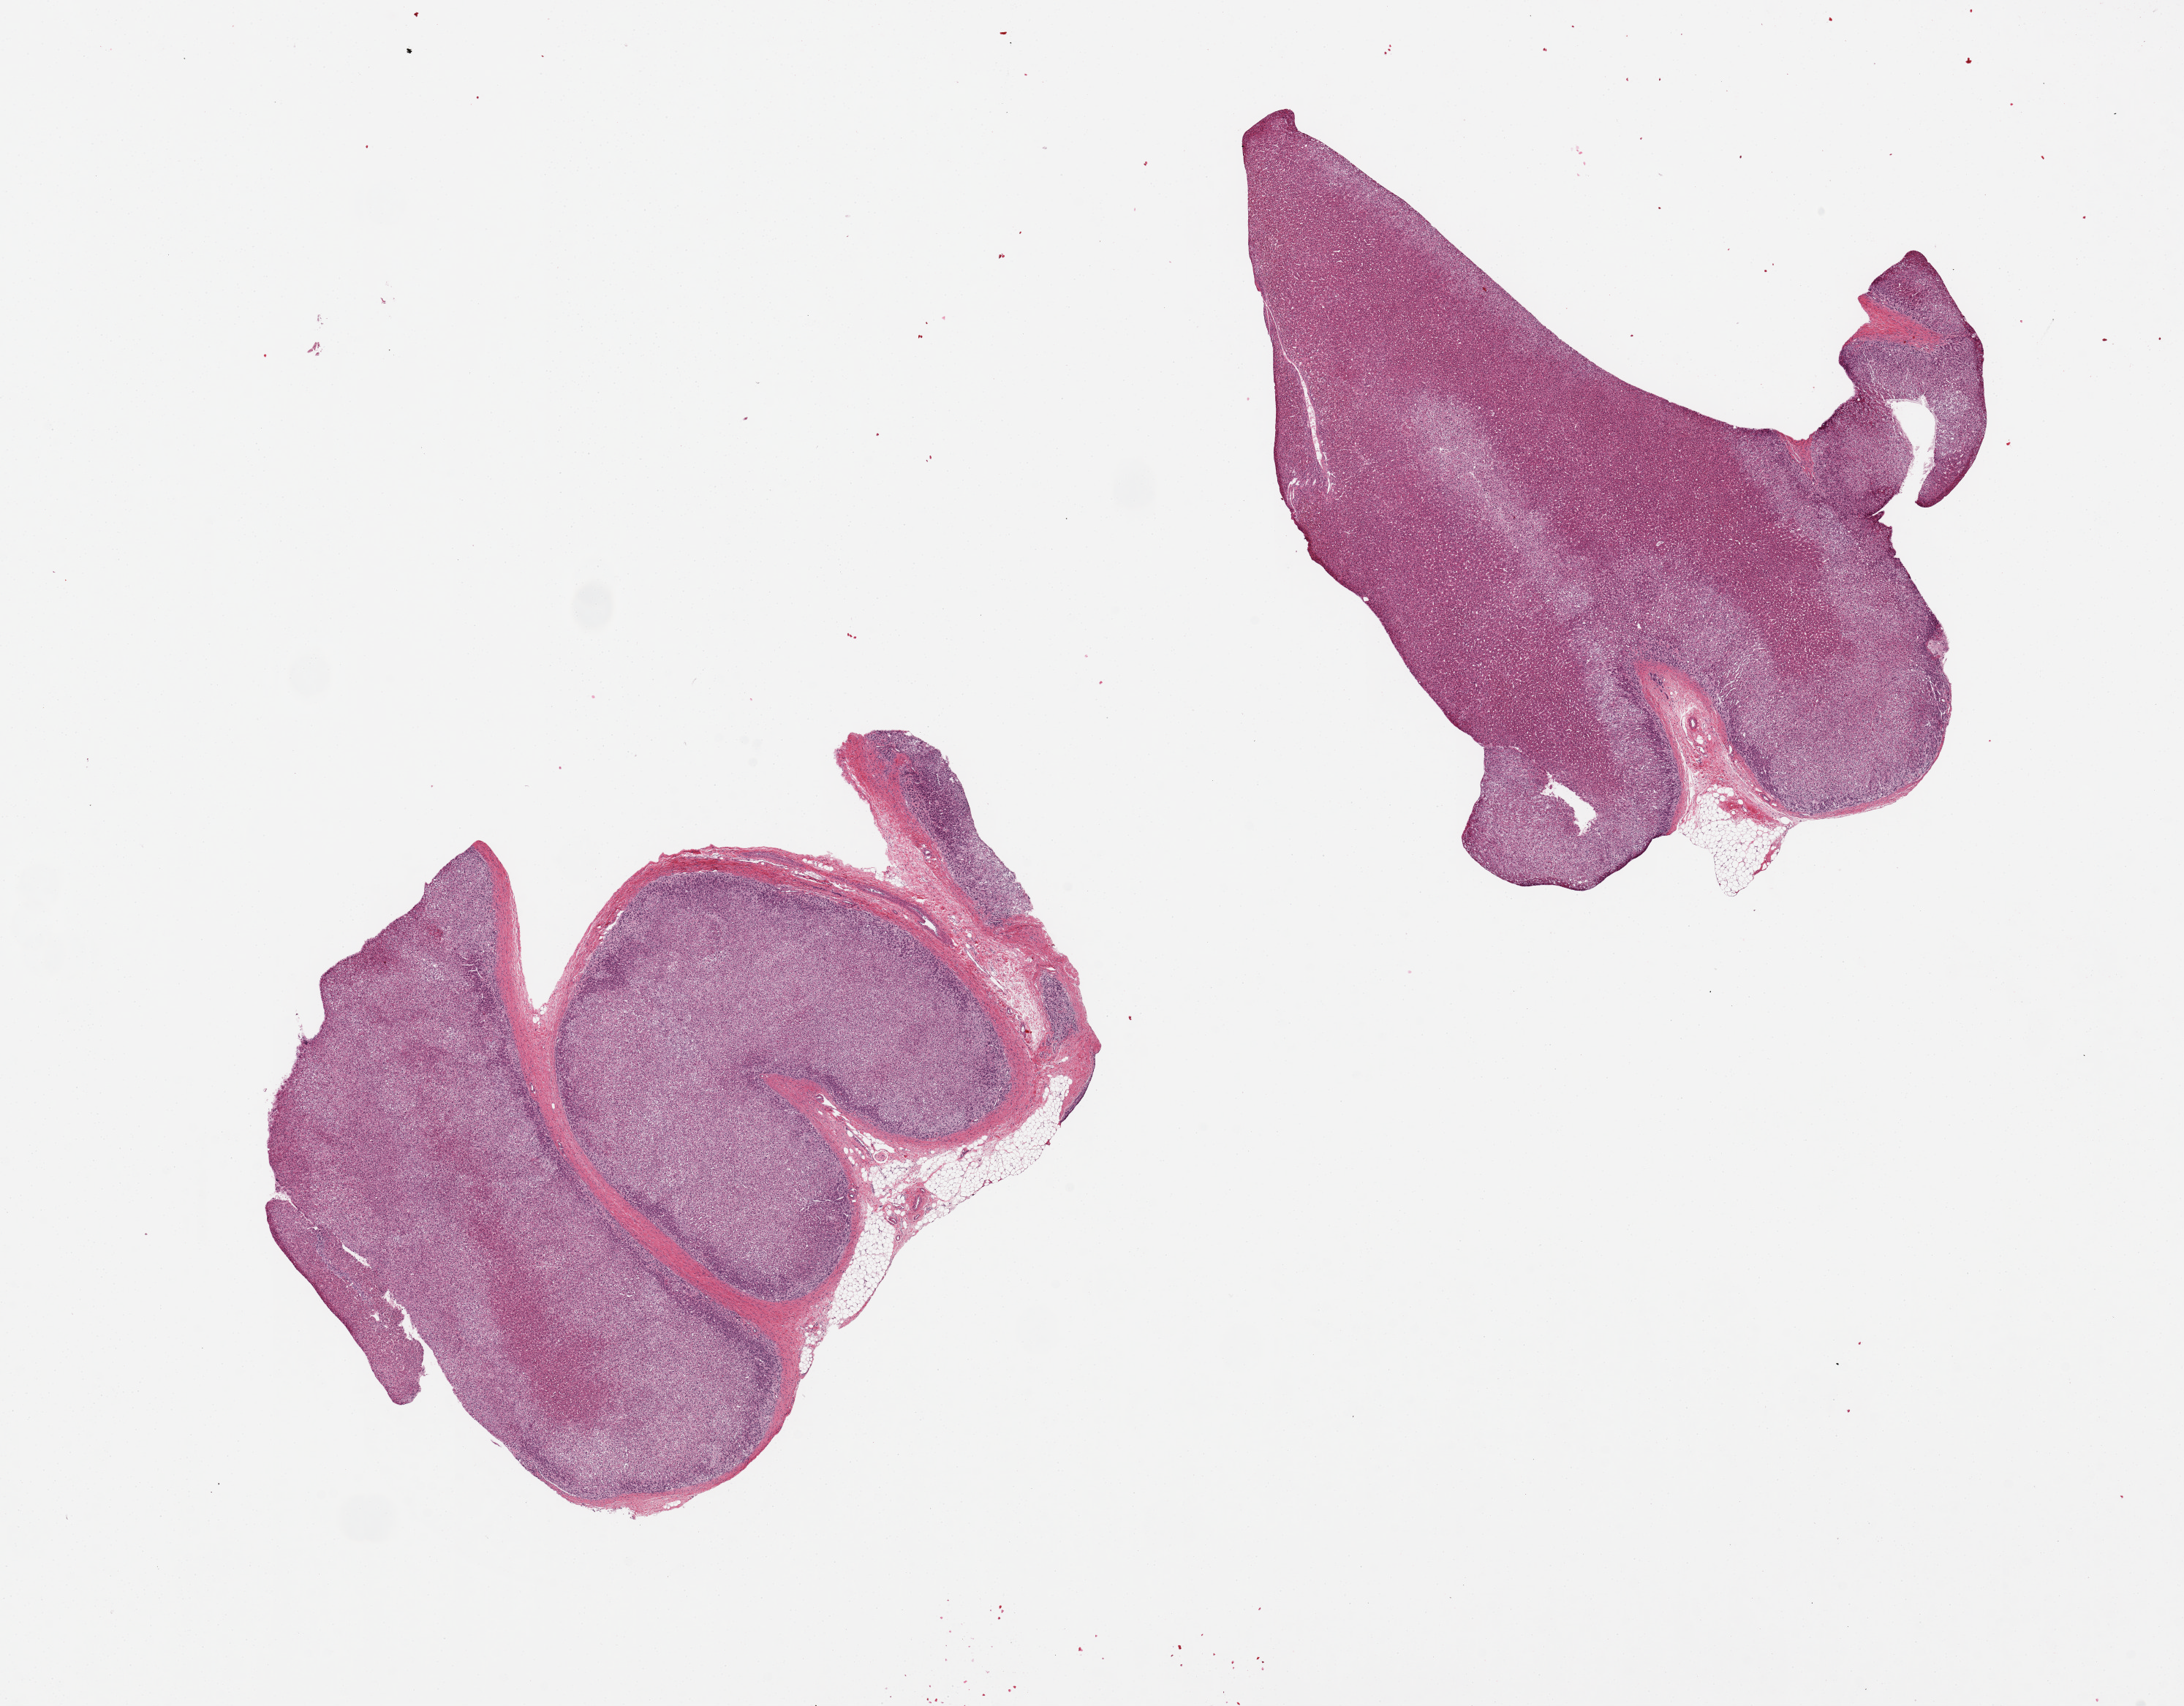
H&E whole-slide image, a low-resolution overview of the entire scanned area, about 23.6 x 18.5 mm.
• specimen: PAXgene-fixed paraffin-embedded (PFPE) section; sampled site (target tissue): adrenal gland; donor tissue sample